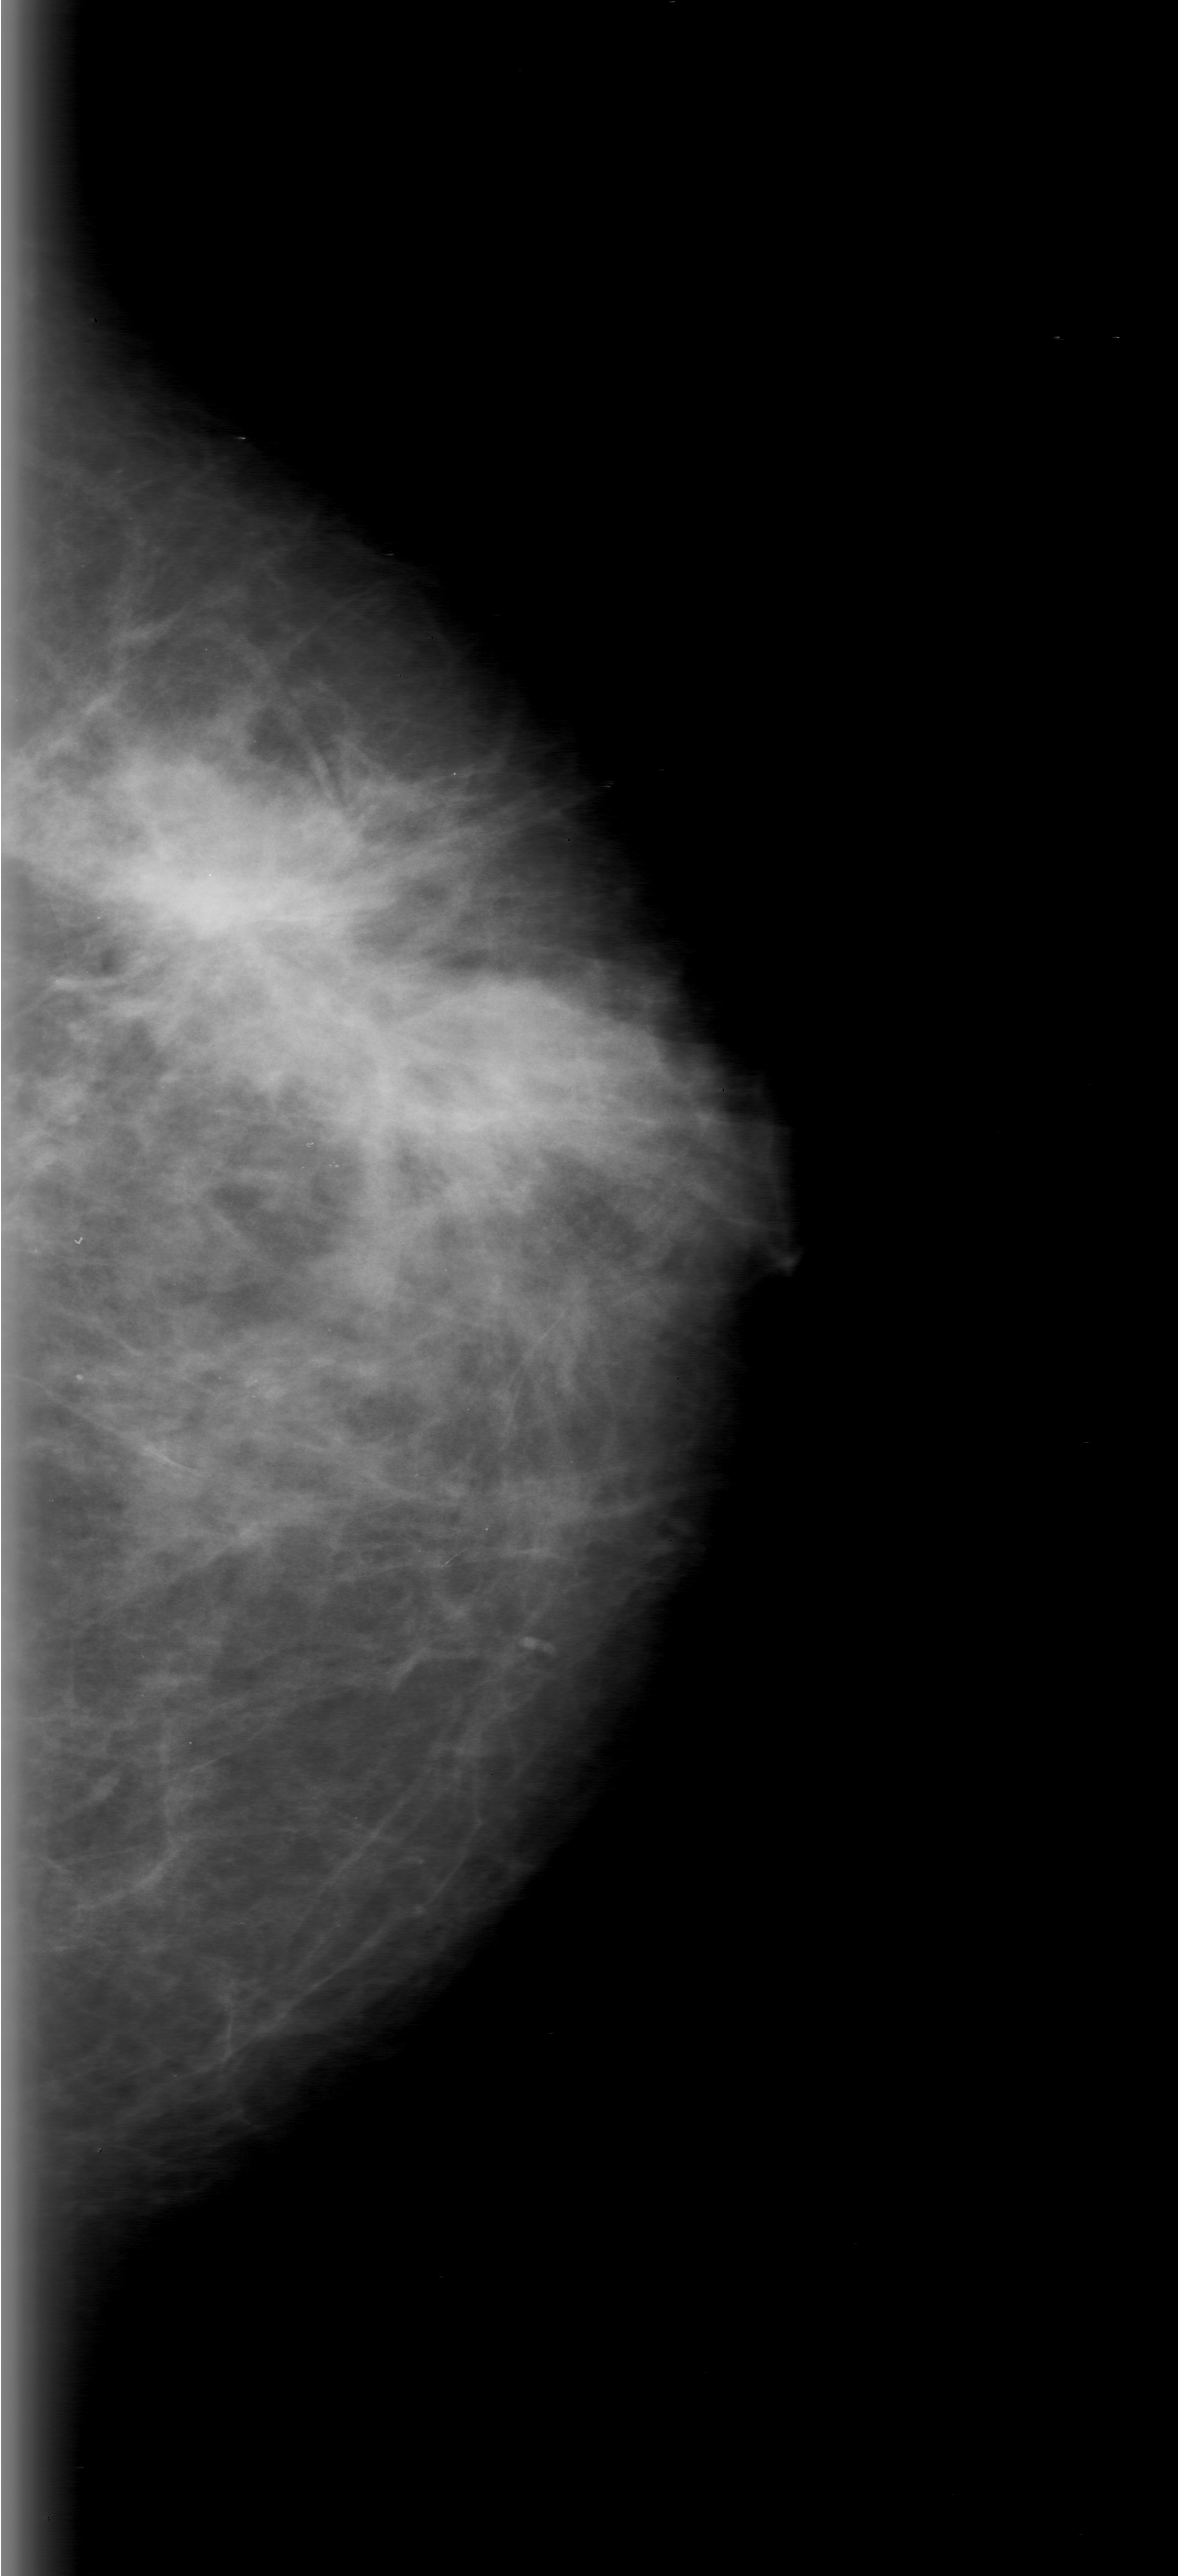
Mammogram (digitized film); left breast; CC view; 1178 × 2576 image matrix.
Marked abnormalities (boxes around the expert regions of interest):
- mass, shape architectural distortion; BI-RADS assessment category 0 (incomplete: needs additional imaging); pathology result (as recorded, not read from the image): malignant: bounding box [x1, y1, x2, y2] px = [98, 783, 340, 1044]